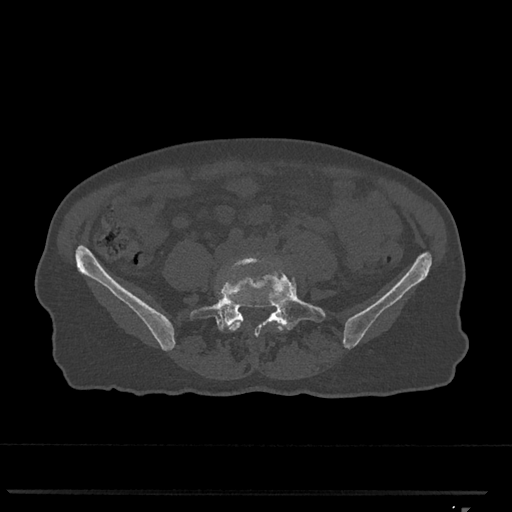
CT including the spine, one axial slice; slice 168 of 793 in the series (ordered by position); reconstruction kernel Br40s/3; 120 kVp; bone window (W 1800 / L 400 HU); 0.5 mm slice thickness; 512 × 512 image matrix, field of view 380 × 380 mm. Female patient, age 62 years. Case-level facts recorded for this patient, not image findings: primary cancer: renal.
Structures marked on this image (semi-automatic segmentation, software-assisted and operator-edited):
- L4 vertebra: bounding box (x1, y1, x2, y2) in pixels: (217, 256, 284, 332)
- L5 vertebra: (189, 262, 326, 336)